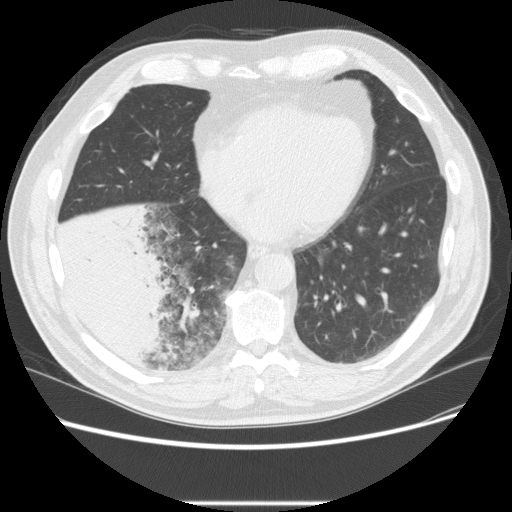
Low-dose screening chest CT, one axial slice; position 80 of 233 along the scan axis; reconstruction kernel STANDARD; 120 kVp; lung window (W 1500 / L -600 HU); 2.5 mm slice thickness; 512 × 512 image matrix.
Structures marked on this image (outlined manually by an expert reader):
- lesion 3 (tumor, lower lobe of right lung): bounding box (x1, y1, x2, y2) in pixels: (54, 205, 175, 366)